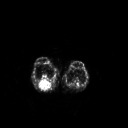
FDG PET of an extremity soft-tissue mass (from a PET/CT study), one axial slice; position 166 of 267 along the scan axis; 3.27 mm slice thickness; 128 × 128 image matrix, field of view 500 × 500 mm. Female patient, age 62 years. Case-level facts recorded for this patient, not image findings: histological type: liposarcoma; site of the primary tumour: right thigh.
Structures marked on this image (expert contour drawn on MRI and transferred to this co-registered scan by the dataset authors):
- gross tumour volume (mass): box from (x=38, y=78) to (x=51, y=90) px